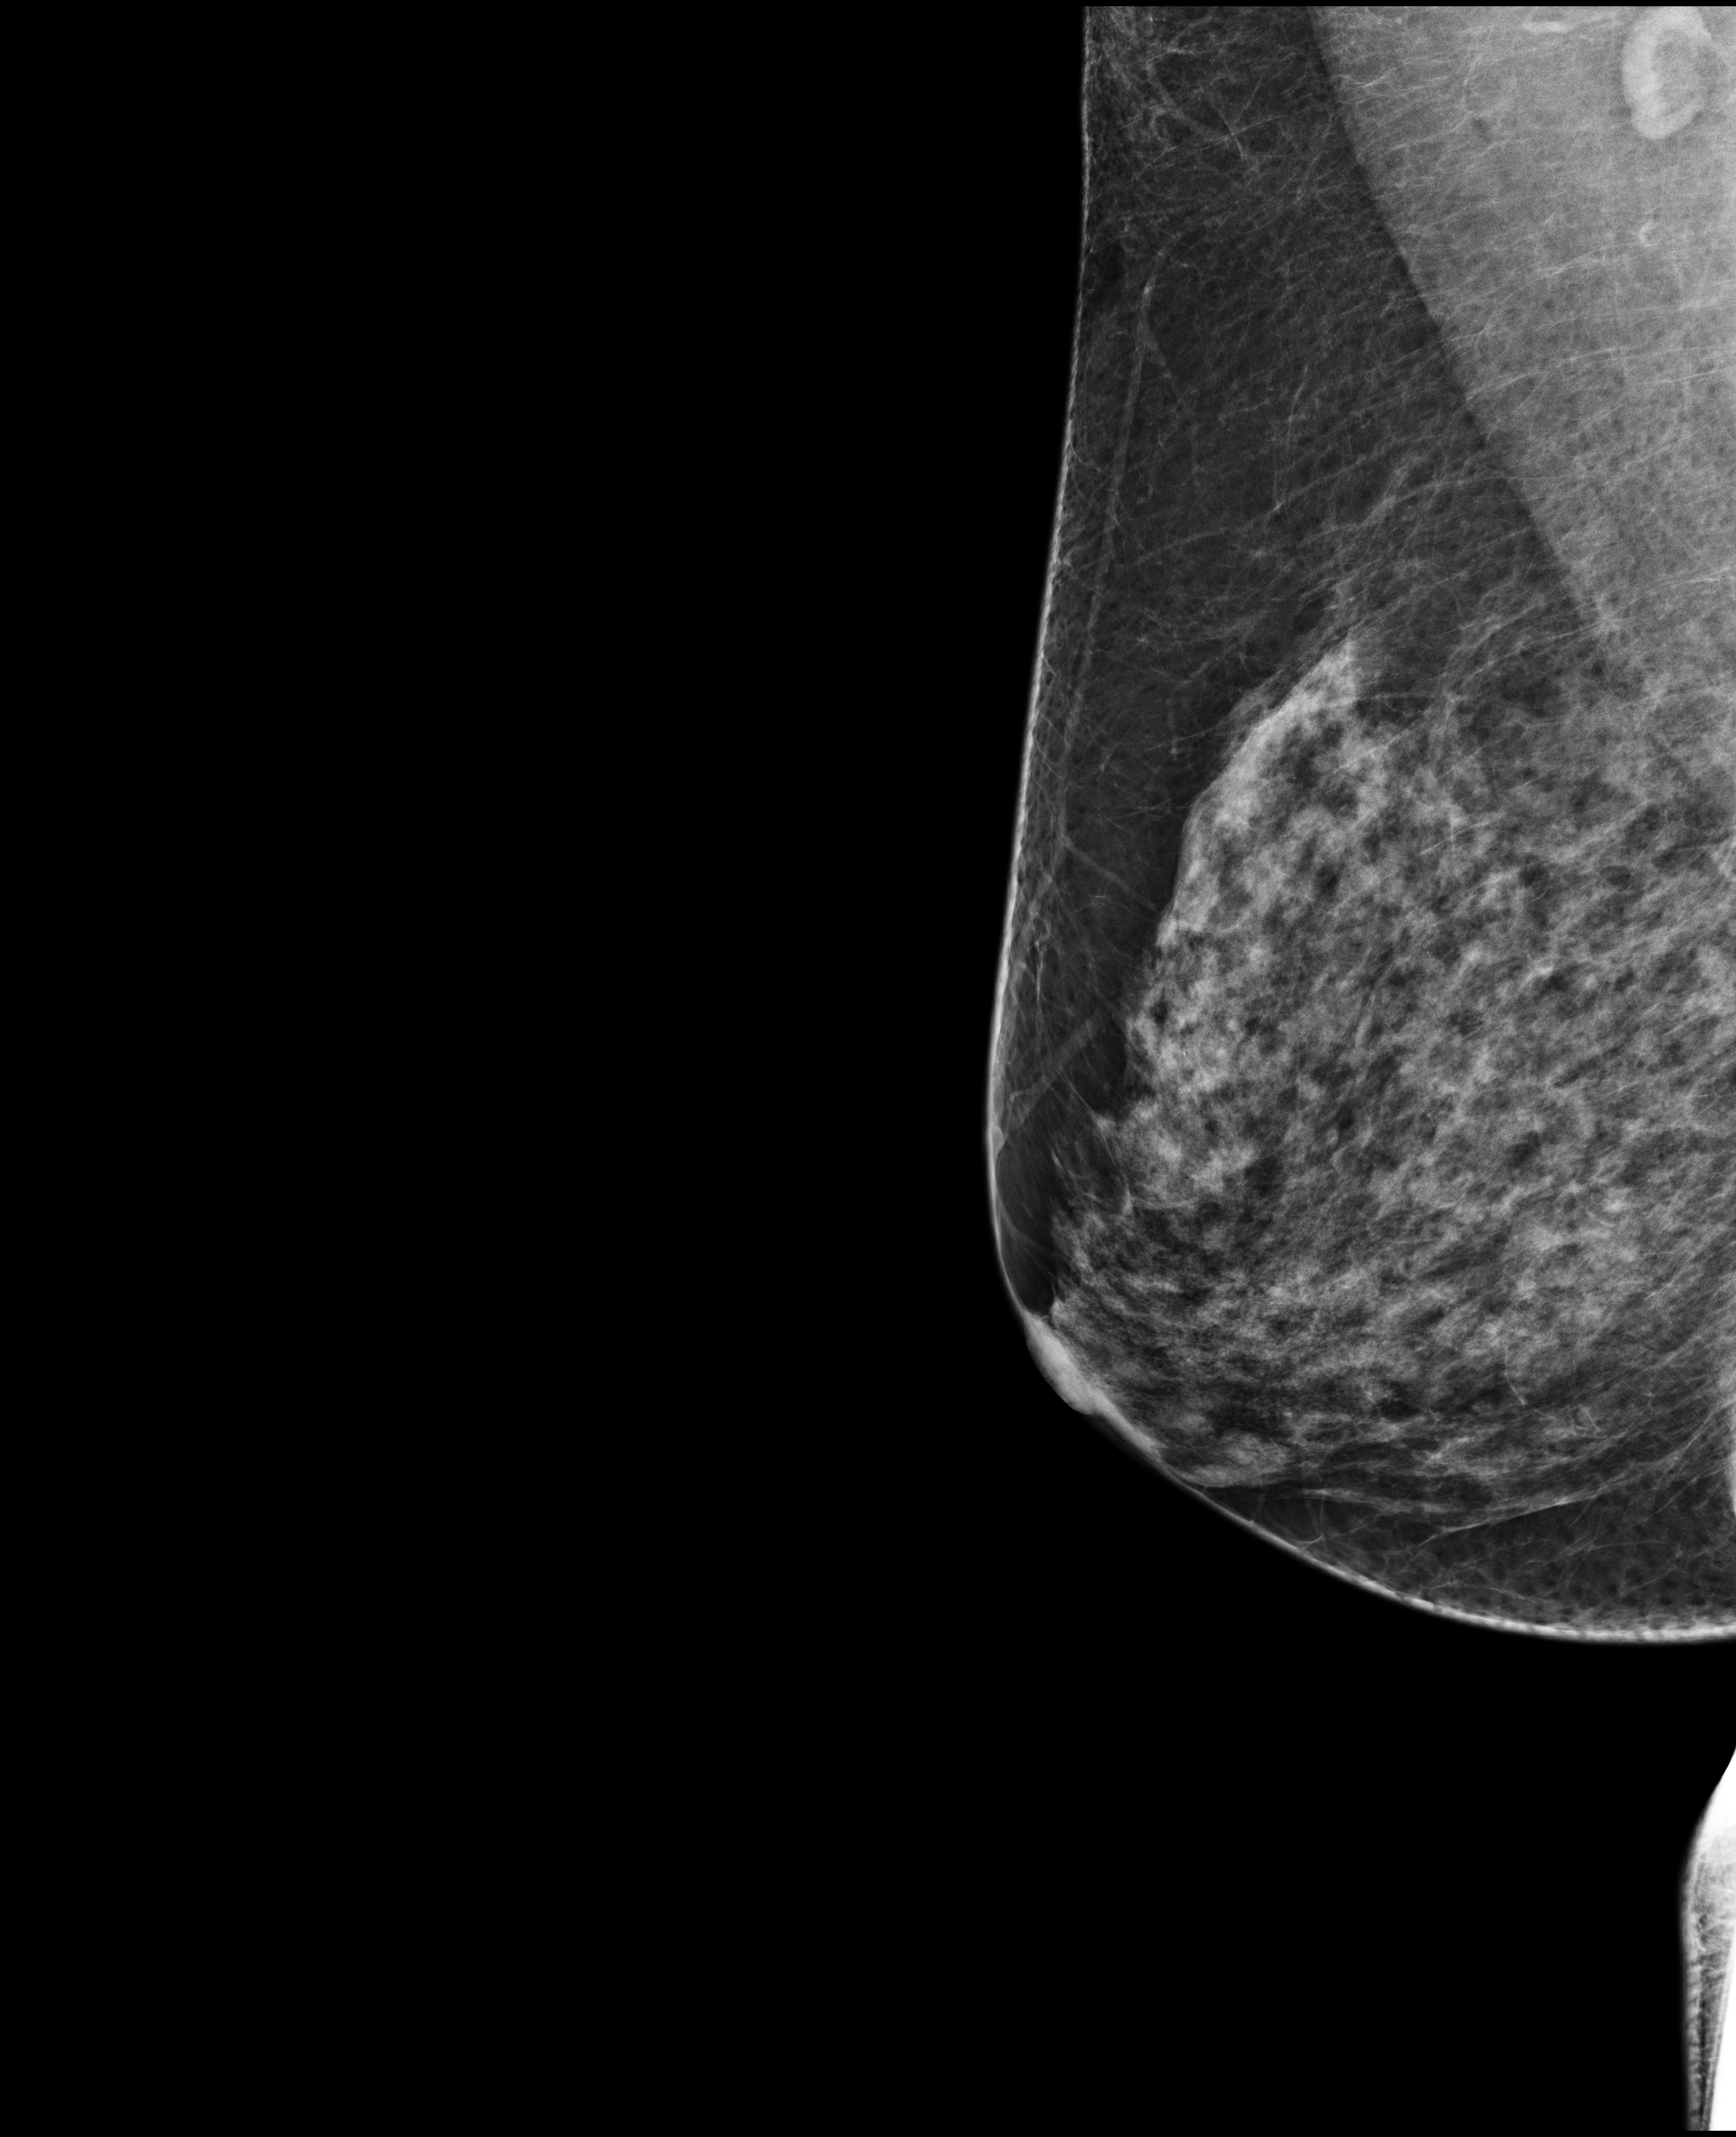
Digital mammogram (FFDM); right breast; medio-lateral oblique projection; annual screening mammography examination. Patient aged 52 years (female).
Final BI-RADS category for the screening round (tomosynthesis exam, both breasts): category 1.